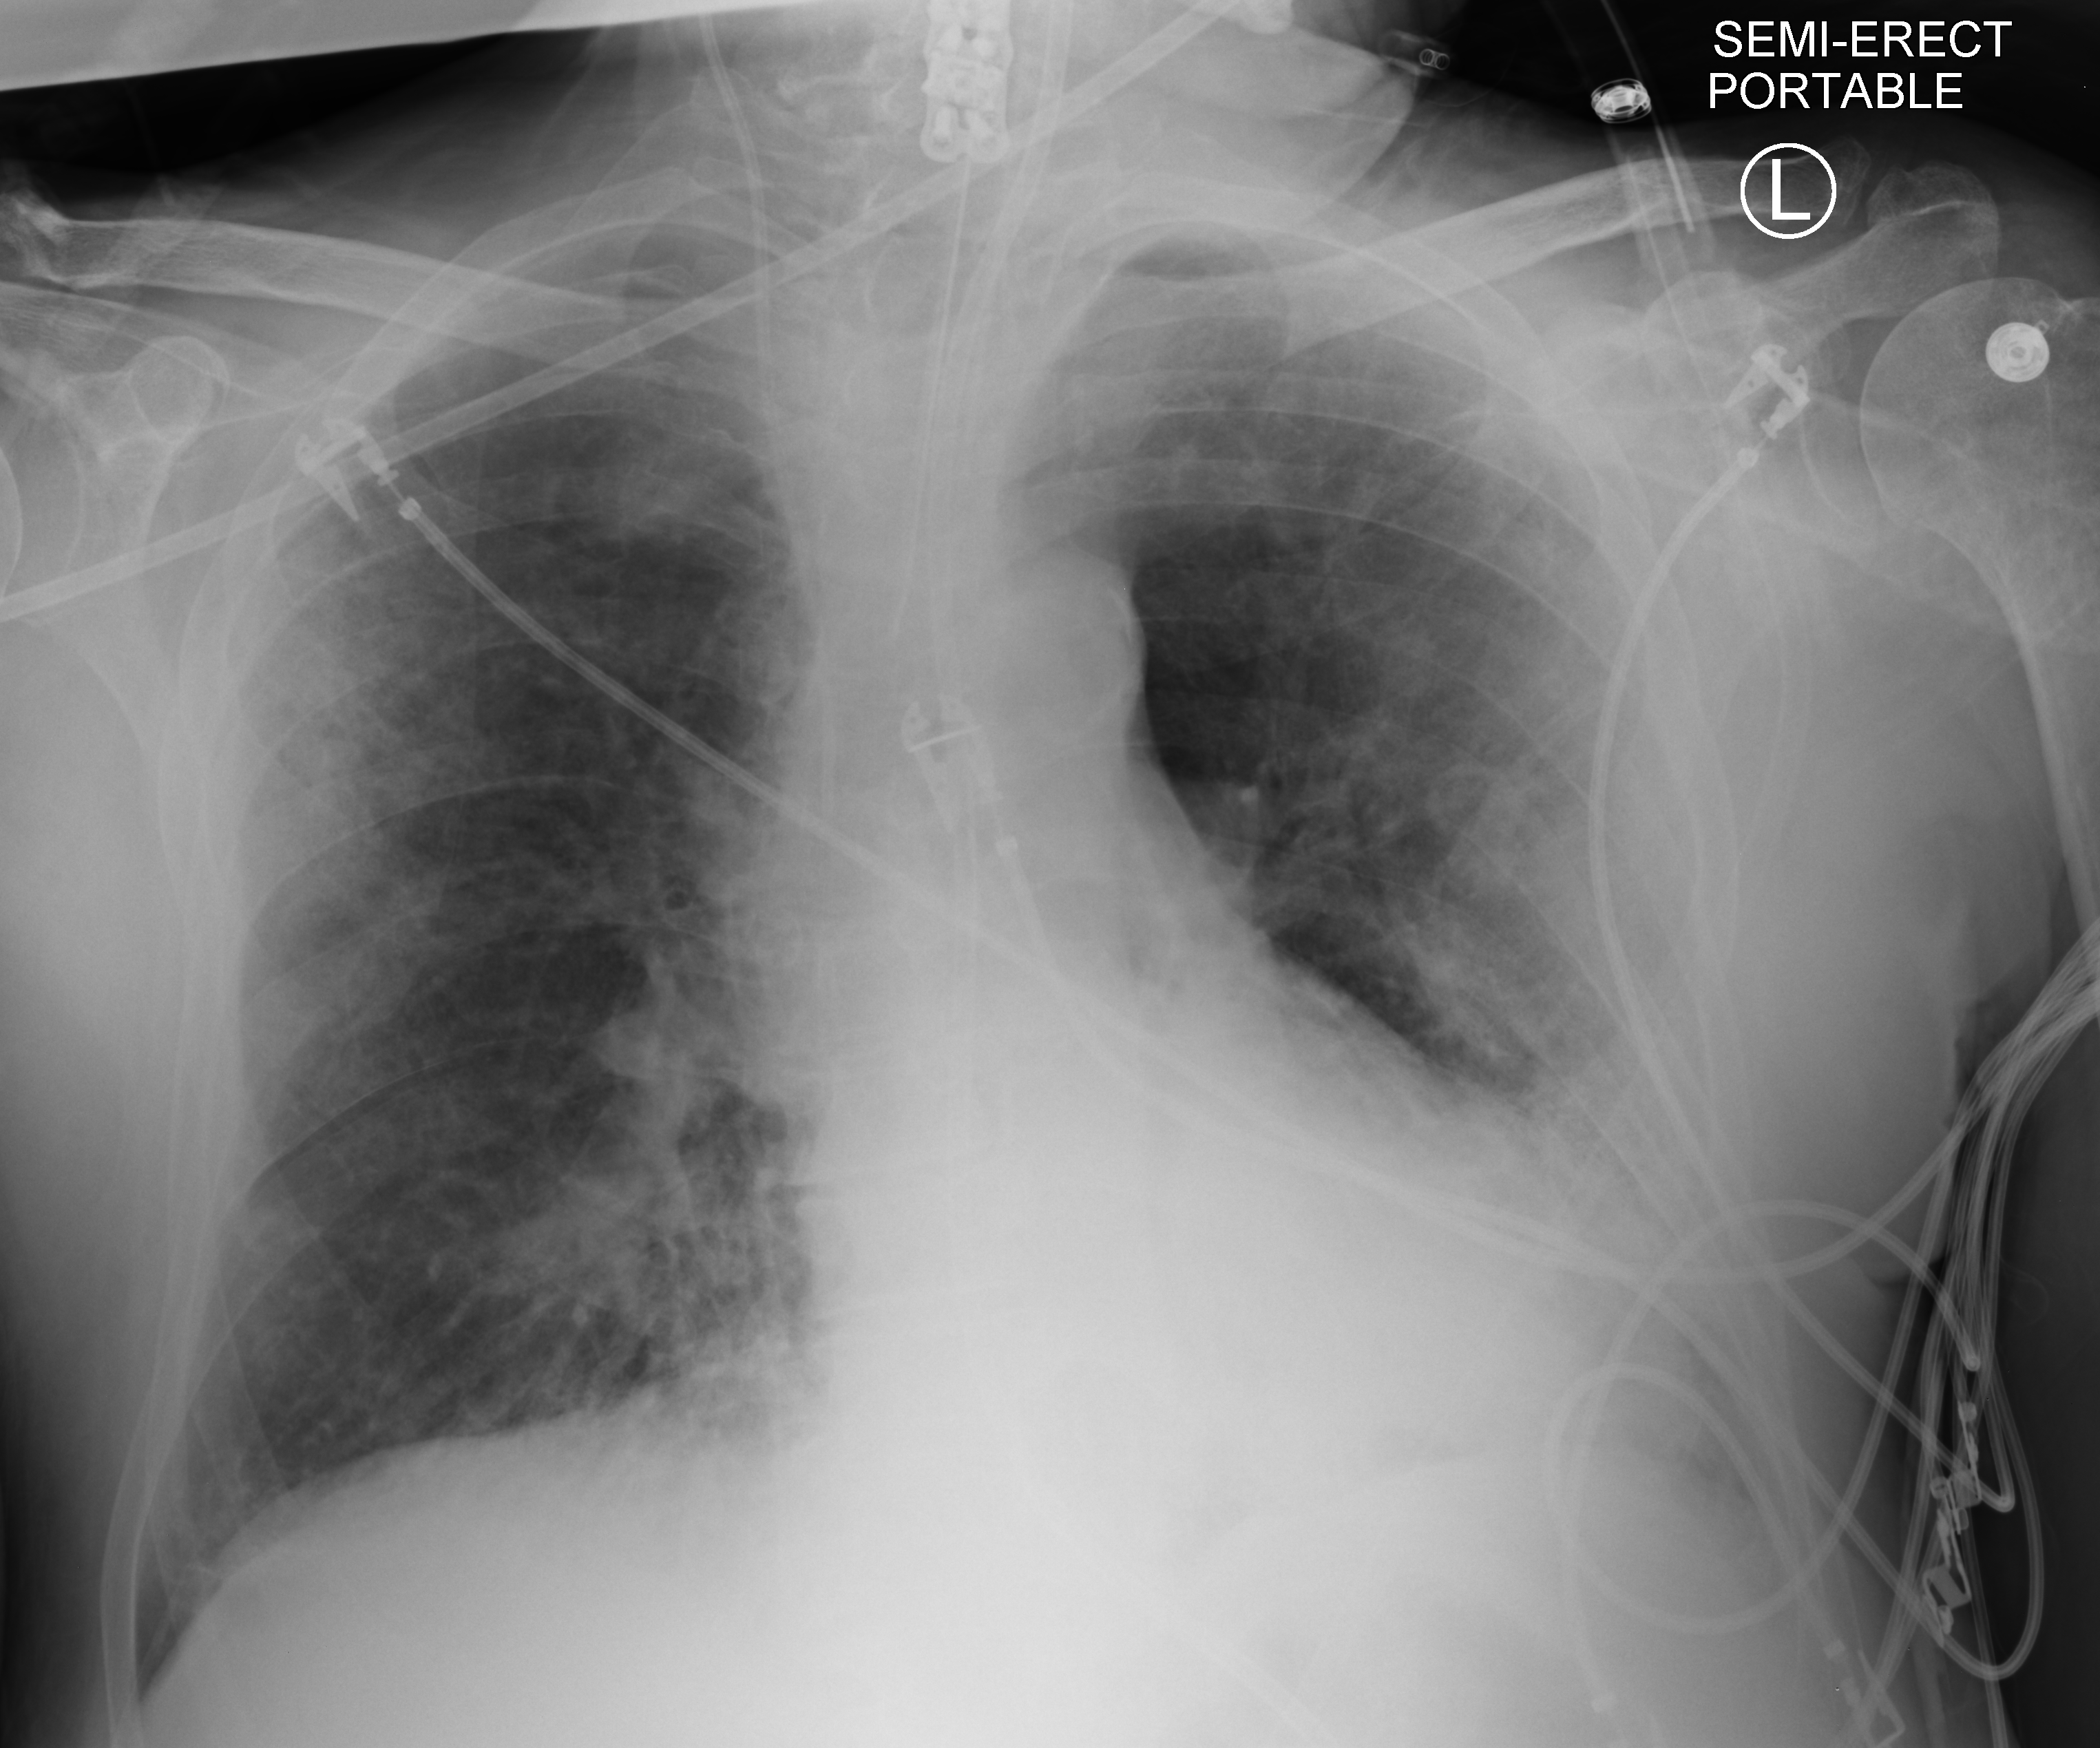
Bedside chest radiograph (computed radiography), anteroposterior (AP) projection. Patient hospitalised with COVID-19; male, aged 75–90 years.
Hospital-stay facts (about this admission, not read from this image; timing relative to this image not recorded): length of hospital stay: 26 days.